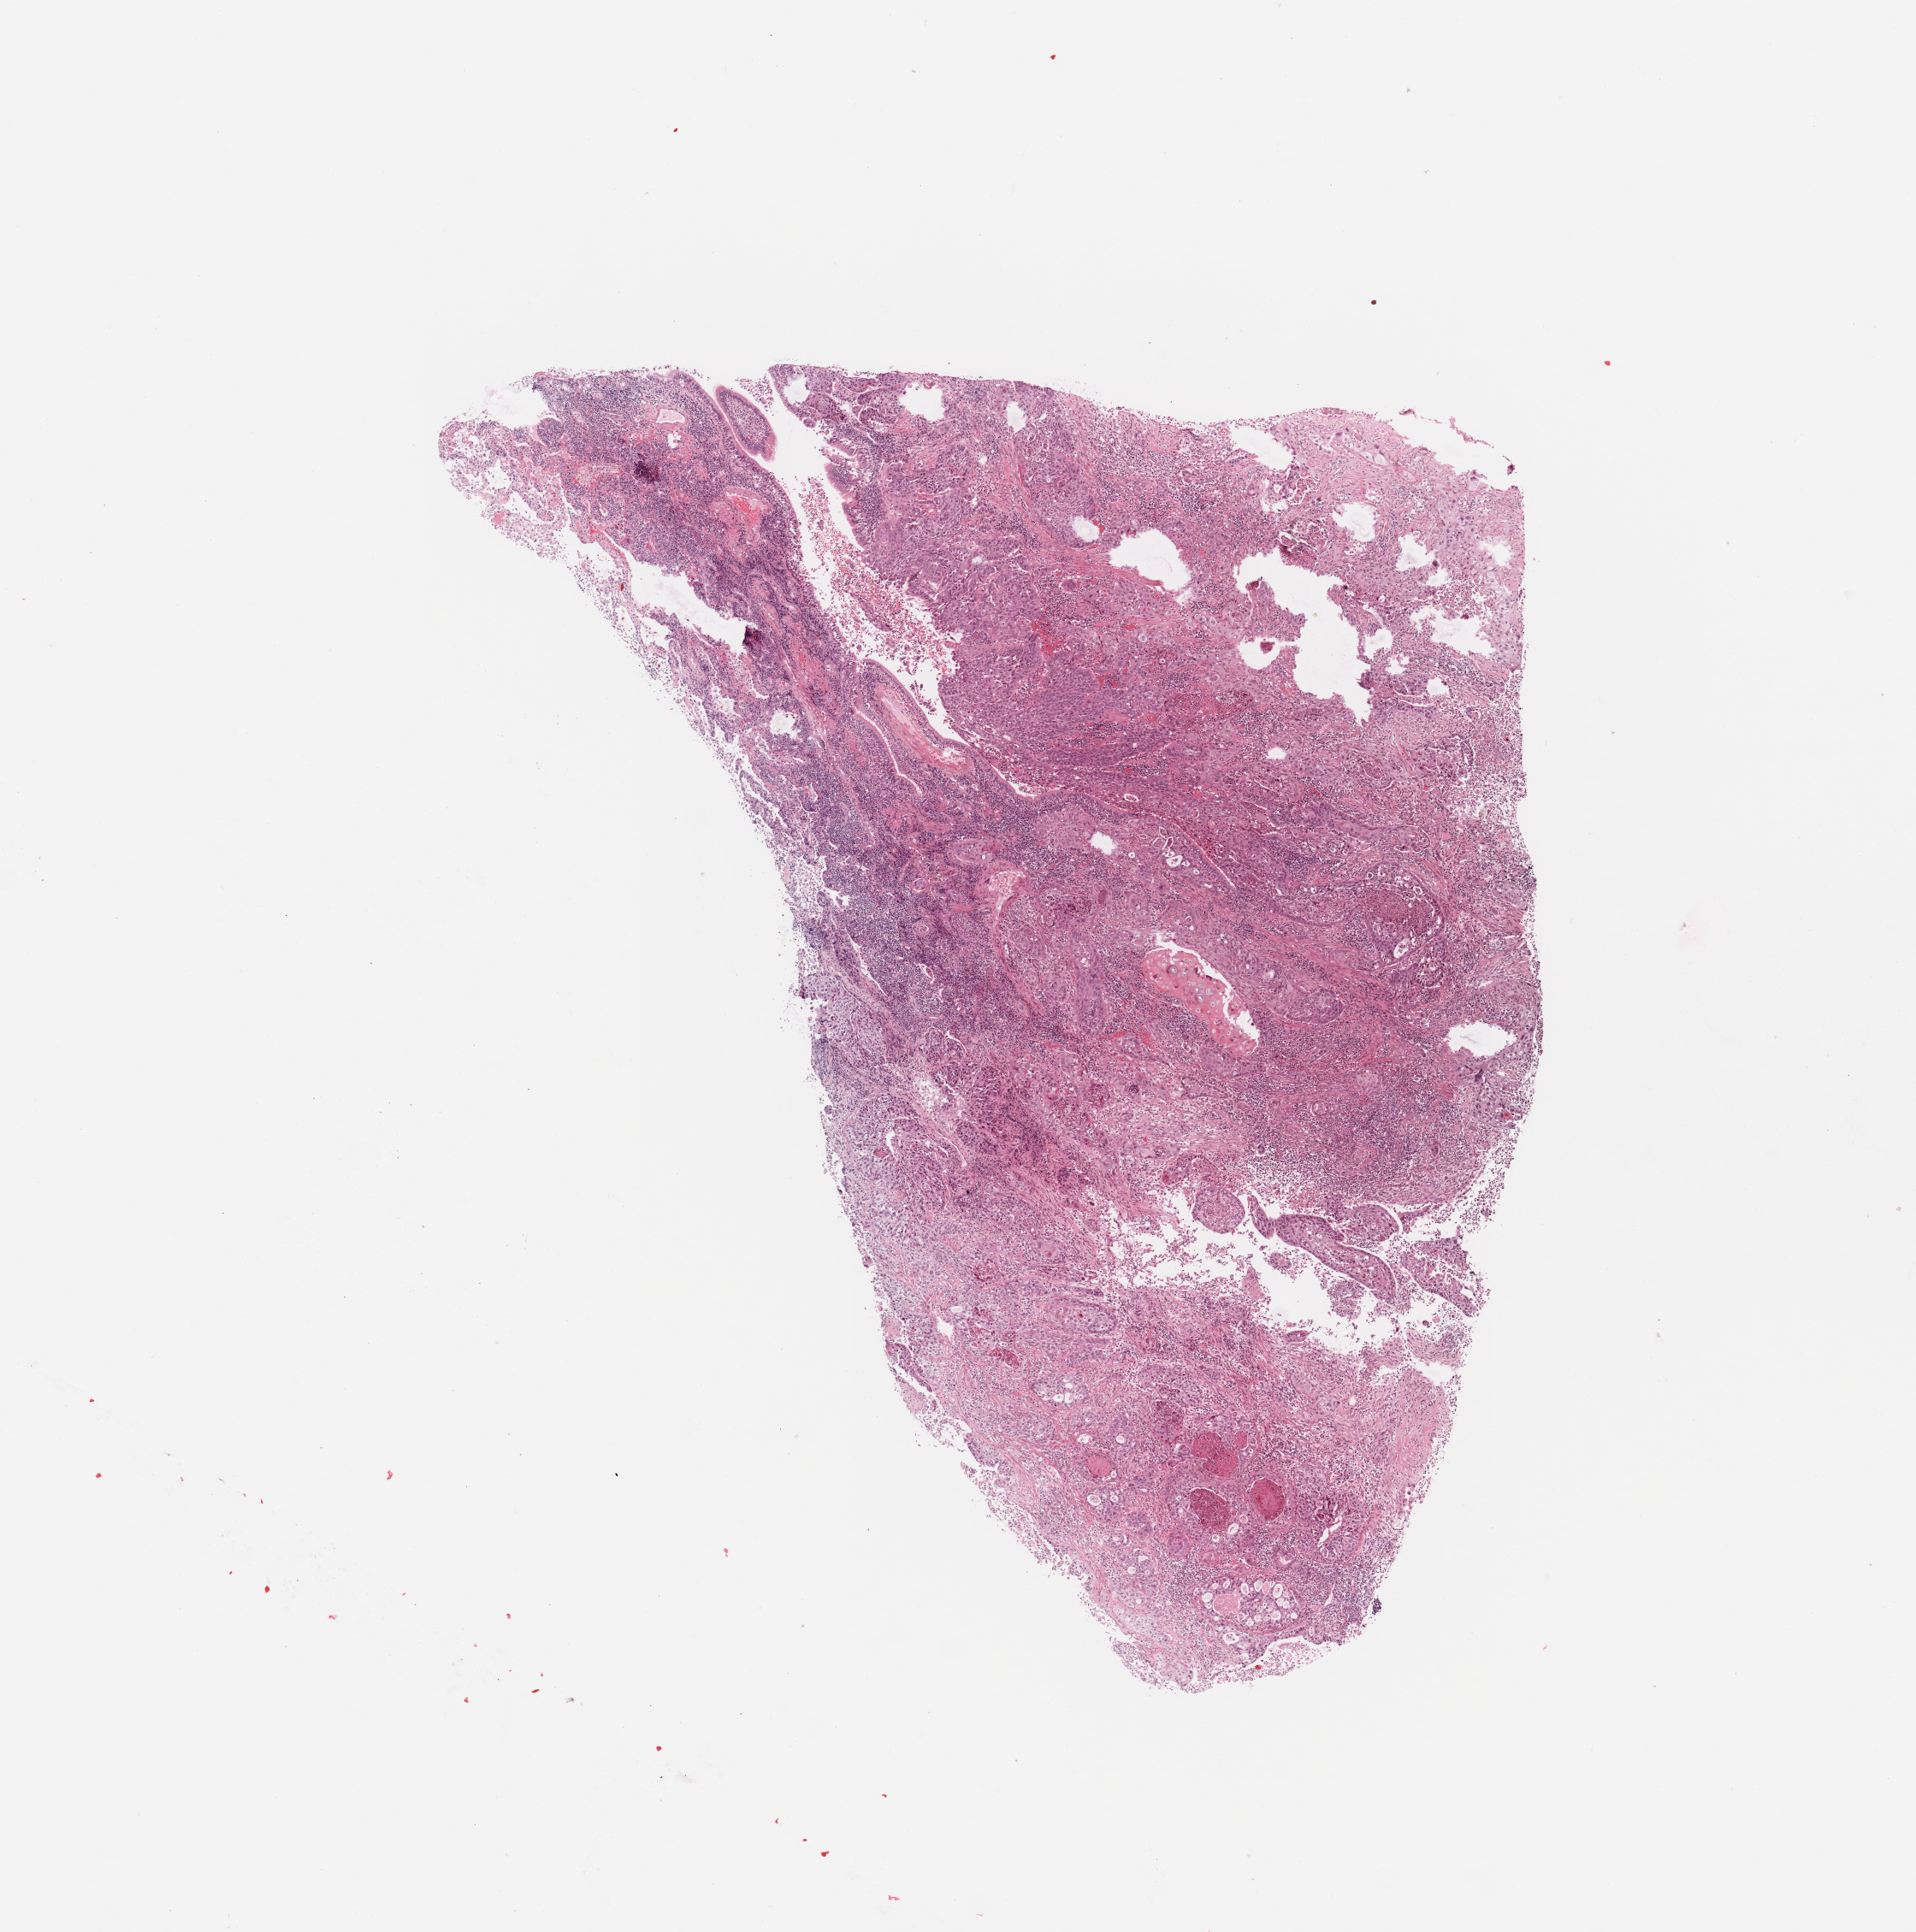
Digitized H&E tissue section (whole slide), whole scanned area (about 8.9 x 8.9 mm, from a 20x scan) shown as a low-resolution overview, tumour tissue sample, sampled site: lung. Male, 63 y/o. Histologic grade: G2 (moderately differentiated). Slide review estimates, as recorded: tumour nuclei 75%, necrosis 5%.
Diagnosis: Squamous cell carcinoma, NOS. AJCC pathologic stage: IIIA. Primary tumour site (as recorded): right lower lobe.